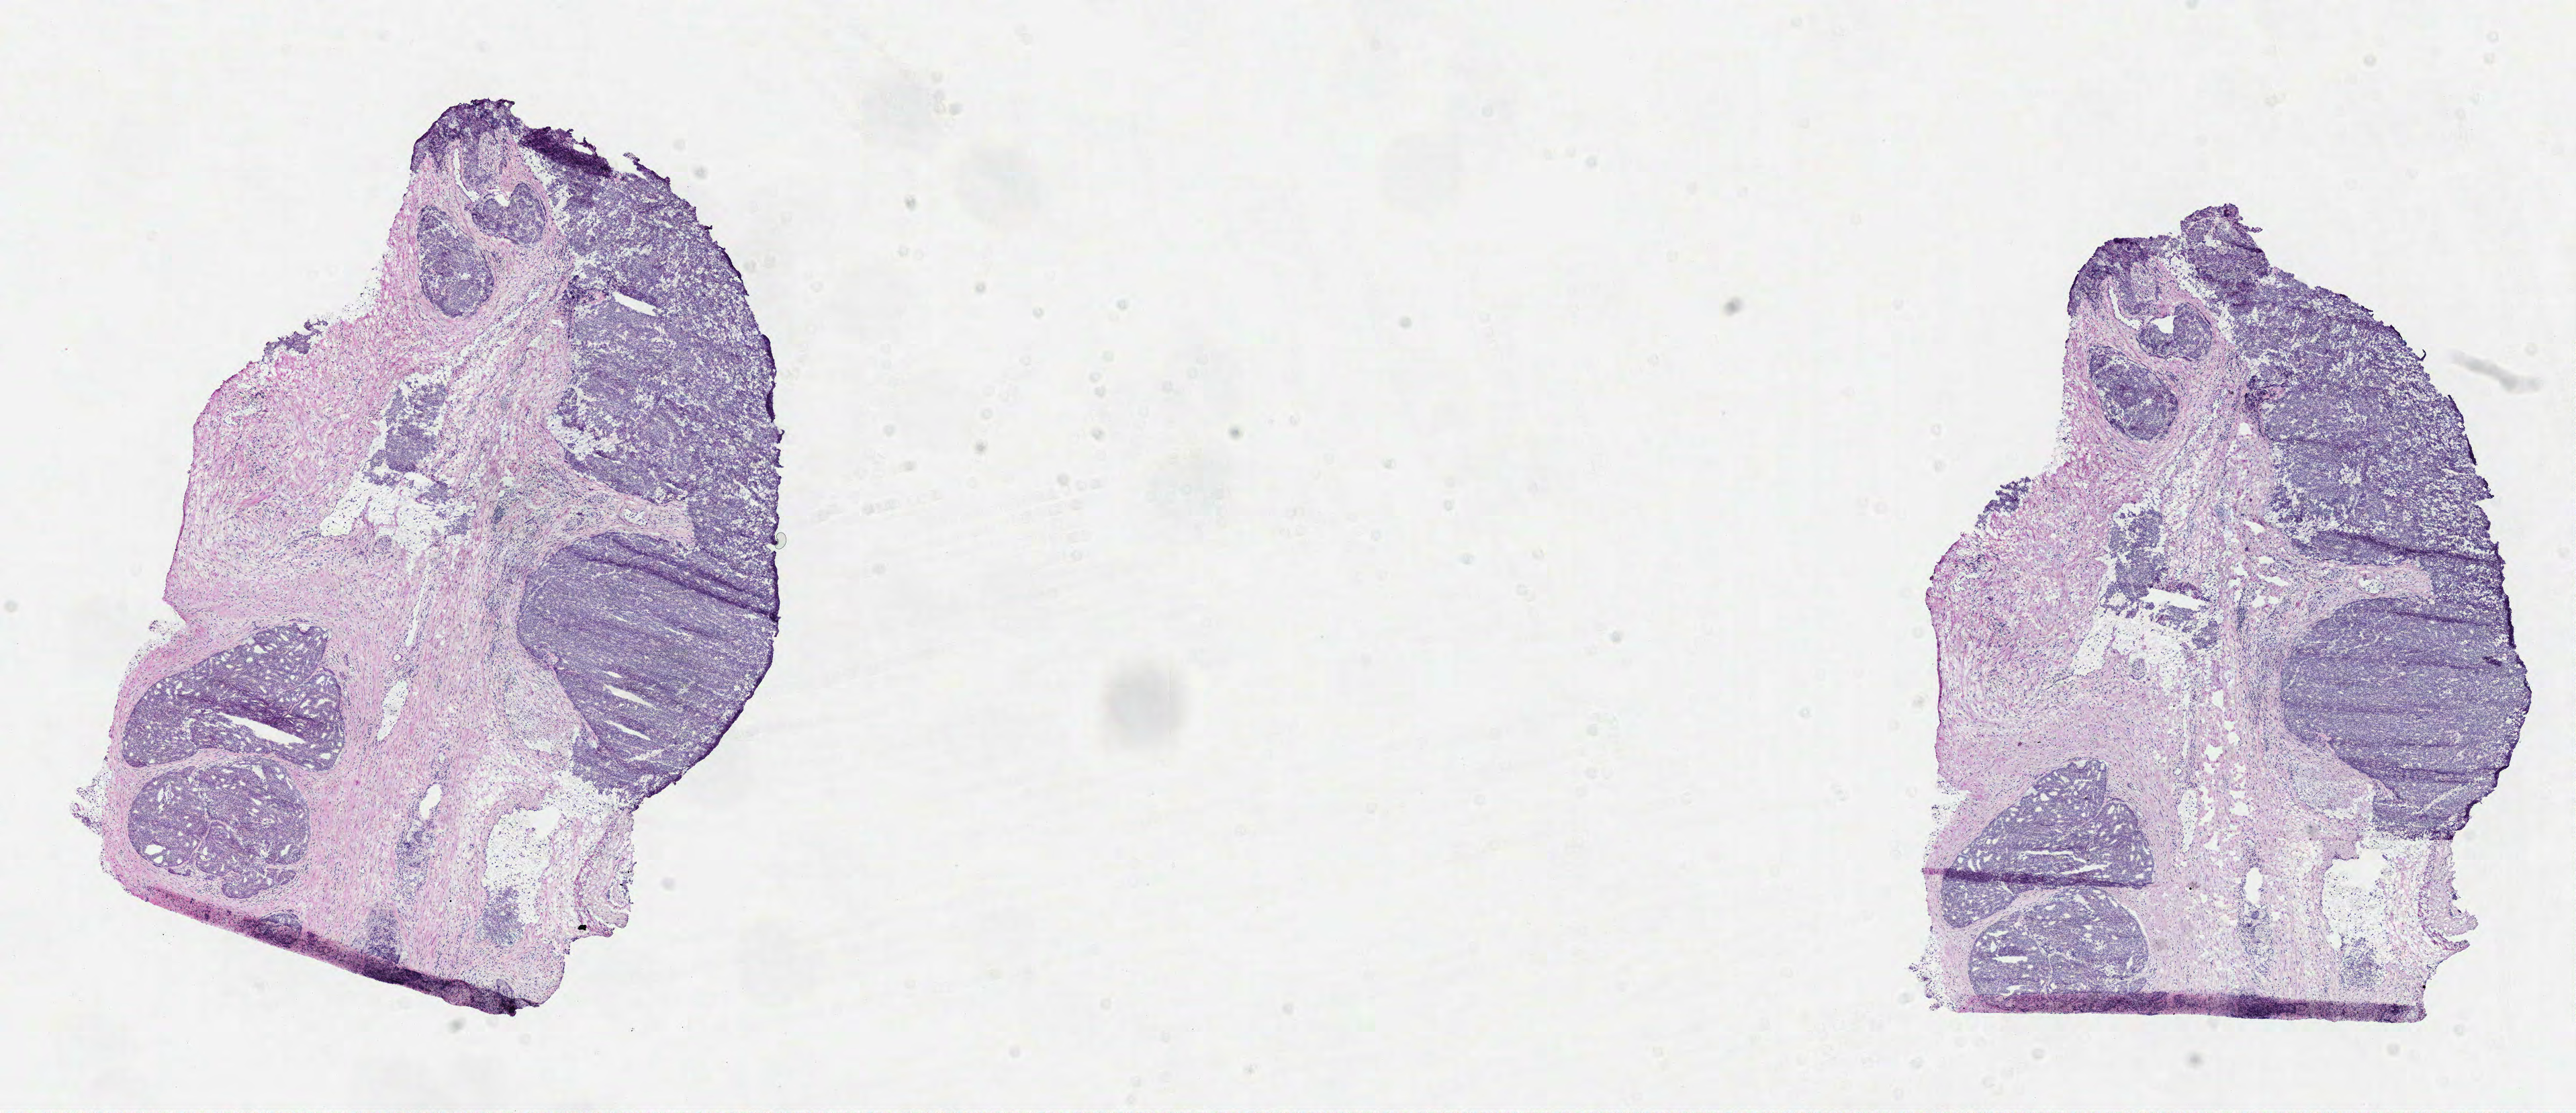
Digitized Hematoxylin and eosin (H&E) stained tissue section (whole slide) — whole scanned area (about 15.5 x 6.7 mm) shown as a low-resolution overview. Formalin-fixed paraffin-embedded (FFPE) diagnostic section. Sample: primary tumour, prostate. Patient: male, age at initial diagnosis 68 years. Gleason score: 10 (5+5).
• lymph nodes positive (case pathology): 1 of 3 examined
• histologic diagnosis: Acinar cell carcinoma (prostate gland)
• laterality: bilateral